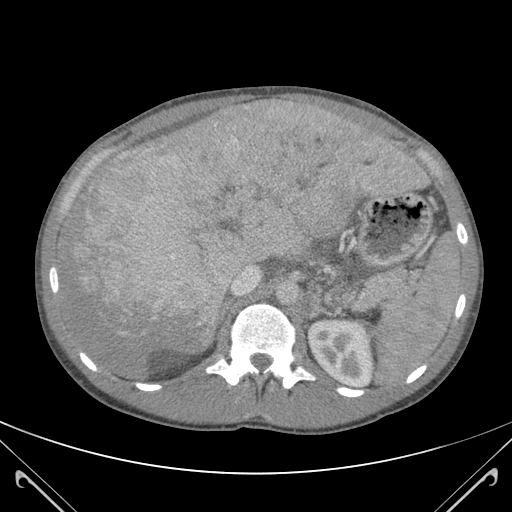
Contrast-enhanced abdominal CT (liver protocol), one axial slice; position 76 of 118 along the scan axis; 120 kVp; soft-tissue window (W 400 / L 40 HU); 512 × 512 image matrix. From the clinical record (not read from this slice): diagnosis: hepatocellular carcinoma (patient treated with transarterial chemoembolisation; whether this scan precedes or follows treatment is not stated here); TNM stage (as recorded): Stage-IIIB; Child-Pugh class: A.
Structures marked on this image (semi-automatic segmentation, software-assisted and operator-edited):
- abdominal aorta: box from (x=276, y=280) to (x=298, y=305) px
- liver parenchyma outside the tumour (the mass and vessels are separate outlines, so this box may not span the whole liver): (x=58, y=103)–(x=420, y=378)
- mass: (x=67, y=103)–(x=426, y=351)
- liver vessels: (x=231, y=106)–(x=285, y=295)